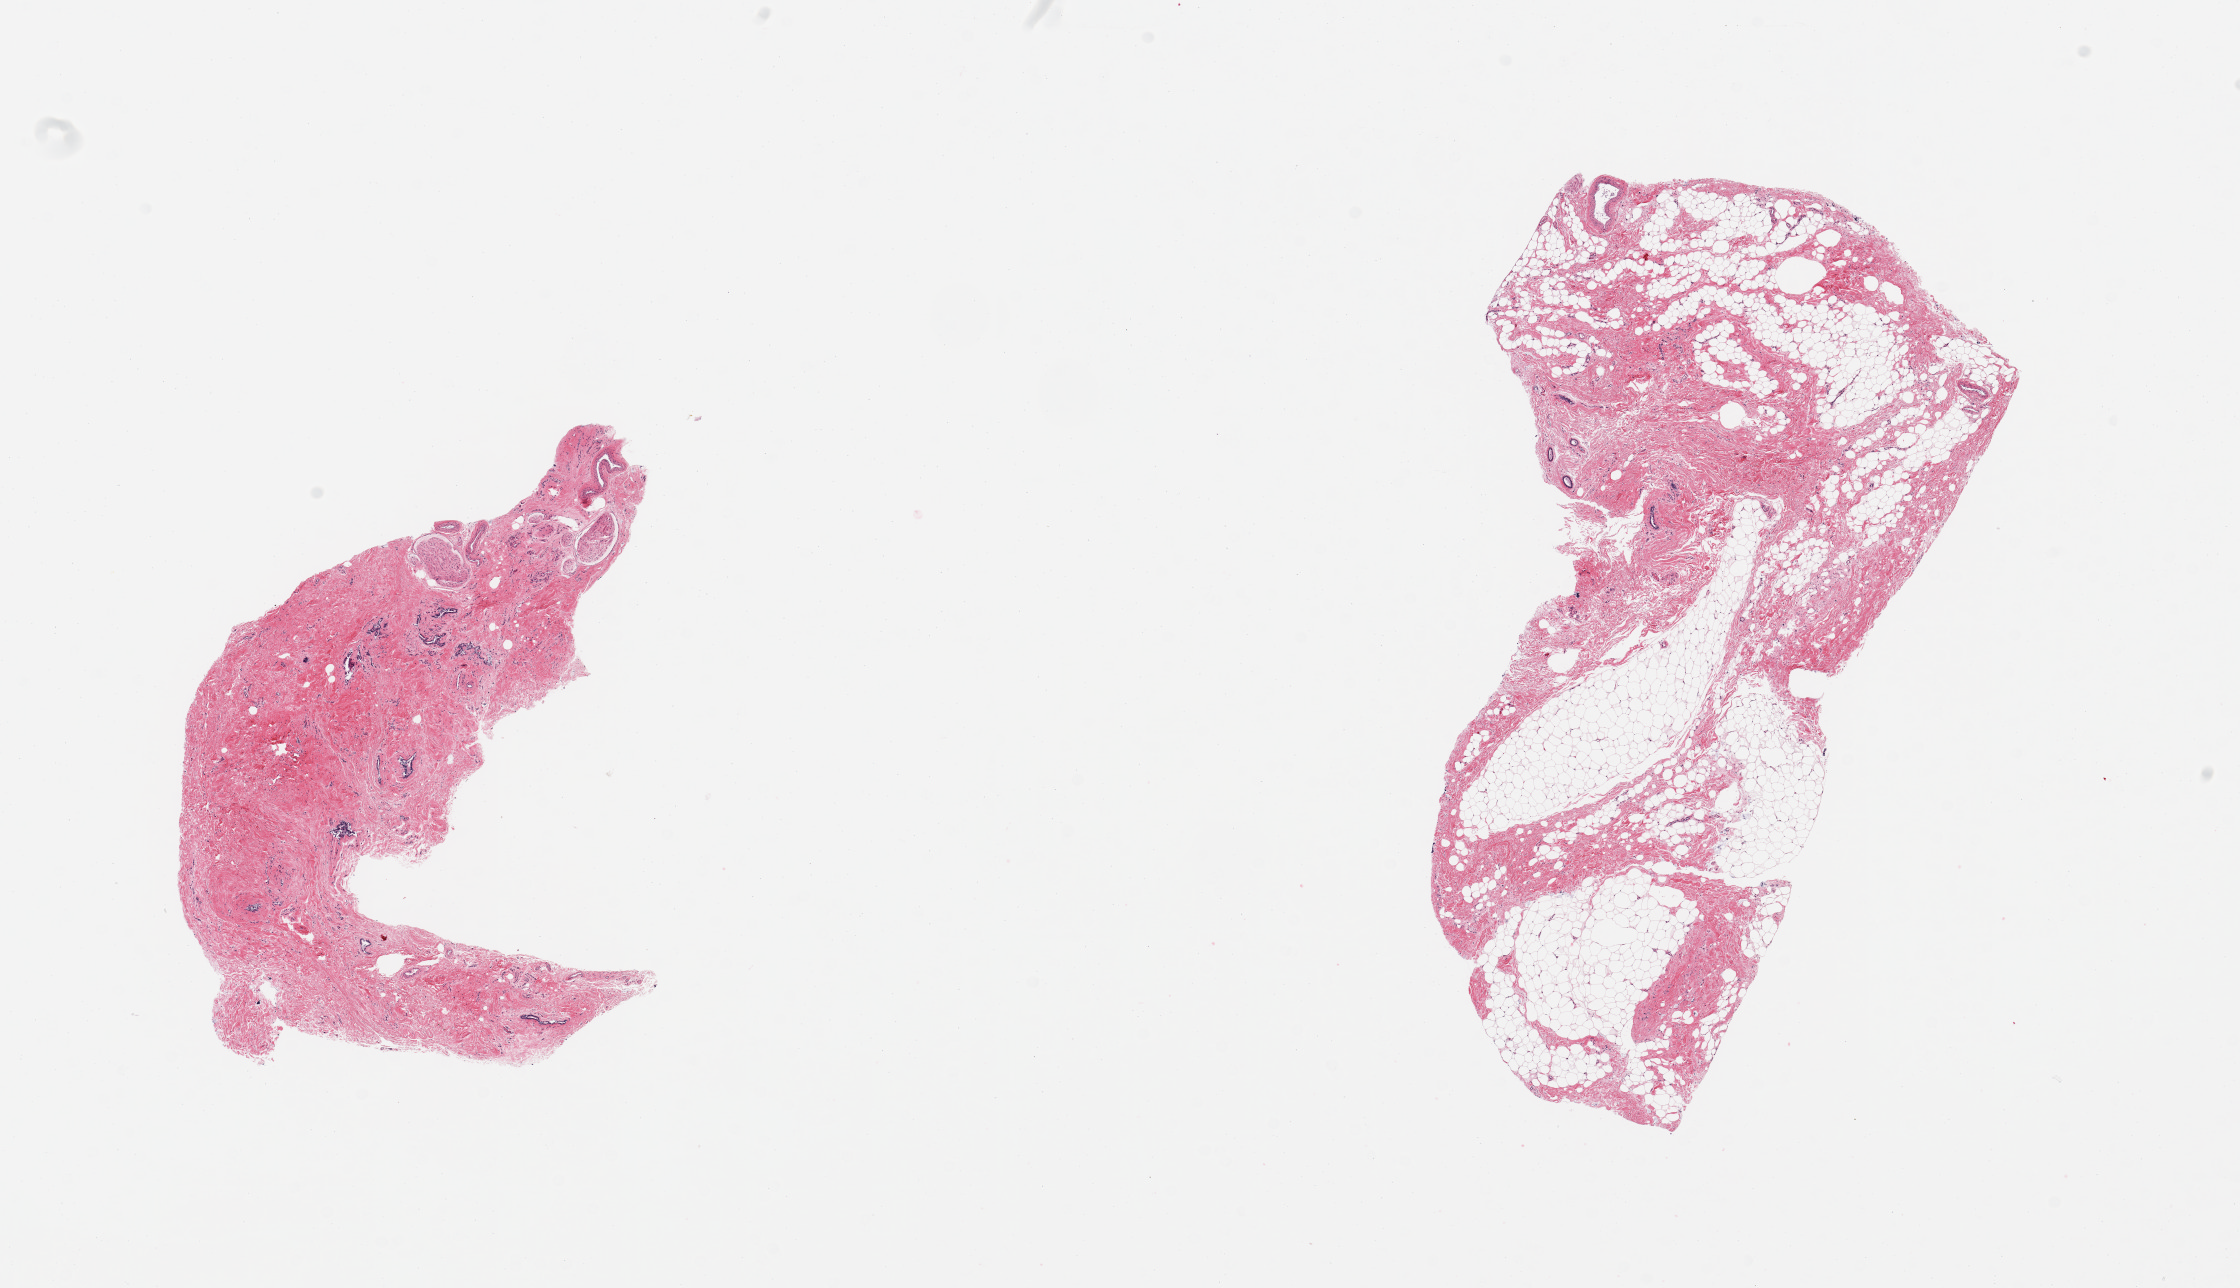
Whole-slide image, haematoxylin and eosin stain, brightfield, whole scanned area (about 17.7 x 10.2 mm, acquisition: 20x scan) shown as a low-resolution overview; PAXgene-fixed, paraffin-embedded tissue; sampled site (target tissue): breast; donor tissue sample. Male donor.
Pathologist's review note for this sample: 2 pieces, fibroadipose elements with a few ductal elements.